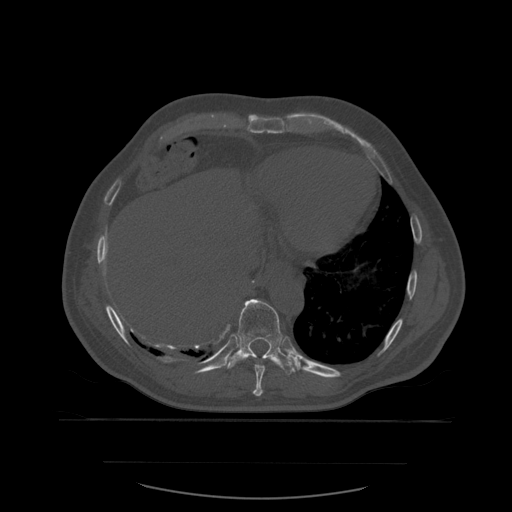
CT including the spine, one axial slice. Bone window (W 1800 / L 400 HU). 1.25 mm slice thickness. 512 × 512 image matrix, field of view 479 × 479 mm. Patient age 71 years. From the clinical record (not read from this slice): primary cancer: lung; vertebrae with lytic lesions (as recorded): T1, T2, L5, S1.
Outlined on this slice (semi-automatic segmentation, software-assisted and operator-edited):
- T10 vertebra: bounding box (x1, y1, x2, y2) in pixels: (227, 299, 298, 375)
- T9 vertebra: (253, 363, 266, 397)